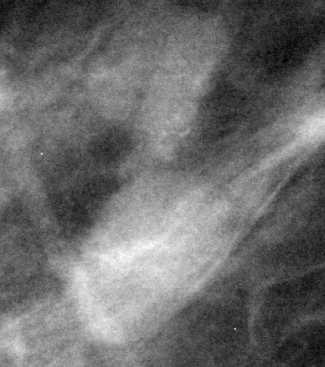
Region of interest cut from a scanned film mammogram (one marked finding); right breast; MLO view.
- Mass, shape oval, margins circumscribed; BI-RADS assessment category 3; subtlety rating 4 on a 1 (subtle) to 5 (obvious) scale; pathology (as recorded): benign.